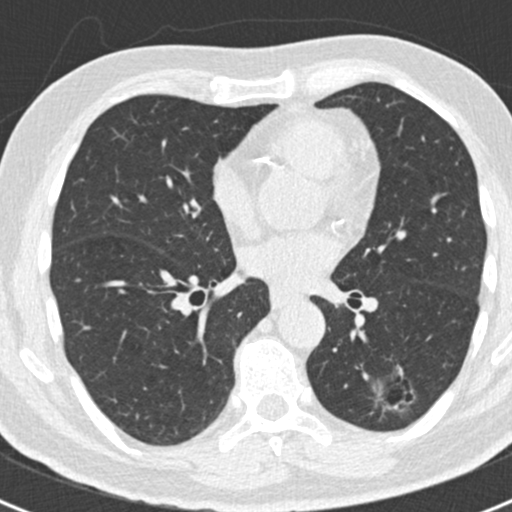
Low-dose screening chest CT, axial slice; baseline annual screen; lung window (W 1500 / L -600 HU); 2 mm slice thickness; standard (soft-tissue) reconstruction kernel (B30f). Male participant, aged 66 years at enrolment.
Lesion marked by an expert reader, bounding box (x1, y1, x2, y2) in pixels: (348, 343, 422, 422). Screening reader's record for this exam (one nodule recorded; not confirmed to be the boxed lesion): non-calcified nodule or mass ≥4 mm, left lower lobe, 43 × 27 mm, smooth margins.